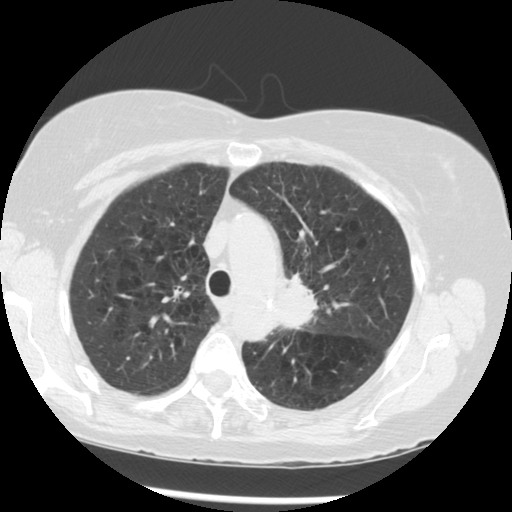
Chest CT (low-dose screening protocol), one axial image. Third screening round (two years after baseline). Lung window (W 1500 / L -600 HU). 2.5 mm slice thickness. 120 kVp. Slice 211 of 283 in the series. Female, age 70 years at enrolment. Current smoker at enrolment.
Lesion marked by an expert reader, box from (x=268, y=264) to (x=361, y=354) px. Reader record for this screening exam (exam-level; its link to the box is not recorded): non-calcified nodule or mass ≥4 mm, left upper lobe, 32 × 26 mm, spiculated (stellate) margins, soft tissue attenuation, pre-existing on the prior screen: yes; interval growth: yes. Official screen result: positive, other. Lung cancer was diagnosed 24 days after this screen: neoplasm, malignant, left upper lobe, stage IIIB (AJCC 6th edition), 40 mm at pathology.